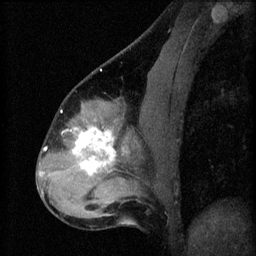
Breast MRI (dynamic contrast-enhanced), one sagittal slice. Slice 28 of 60 in the series (ordered by position). 3 images stored at this slice position (order not interpretable as contrast timing). 1.5 T. TE 4.2 ms, TR 8.2 ms. 2.3 mm slice thickness. 256 × 256 image matrix. Female patient, age 37 years.
Structures marked on this image (semi-automatic segmentation, software-assisted and operator-edited):
- analysis volume of interest (the breast-tissue region the enhancement analysis was run in; not a lesion): box from (x=67, y=120) to (x=122, y=179) px
- tumour enhancement mask (voxels above the 70 % enhancement threshold inside the analysis volume of interest): (x=68, y=126)–(x=116, y=175)